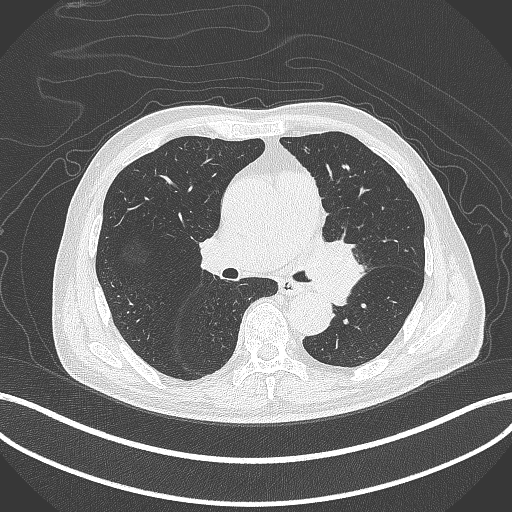
Chest CT, one axial slice; position 245 of 417 along the scan axis; 120 kVp; lung window (W 1500 / L -600 HU); 1 mm slice thickness; 512 × 512 image matrix, field of view 400 × 400 mm. Patient: male, 77 years. Case-level facts recorded for this patient, not image findings: clinical TNM (as recorded): T3 N1 M0.
Outlined on this slice (rectangle marked by the reading radiologist):
- lung tumour (recorded histology: adenocarcinoma): bounding box (x1, y1, x2, y2) in pixels: (301, 241, 366, 309)